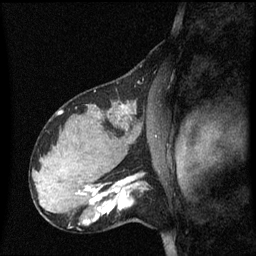
Breast MRI (dynamic contrast-enhanced), one sagittal slice. Position 38 of 60 along the scan axis. Dynamic contrast-enhanced series, image 2 of 3 at this slice position (ordered by acquisition). 1.5 T. TE 4.2 ms, TR 8.4 ms. 2.1 mm slice thickness. 256 × 256 image matrix. Patient: female, 31 years. From the clinical record (not read from this slice): setting: breast cancer imaged before/during neoadjuvant chemotherapy; receptor status: HR-positive, HER2-negative.
Annotated regions visible in this slice (semi-automatic segmentation, software-assisted and operator-edited):
- analysis volume of interest (the breast-tissue region the enhancement analysis was run in; not a lesion): box from (x=98, y=175) to (x=150, y=226) px
- tumour enhancement mask (voxels above the 70 % enhancement threshold inside the analysis volume of interest): (x=98, y=177)–(x=137, y=219)